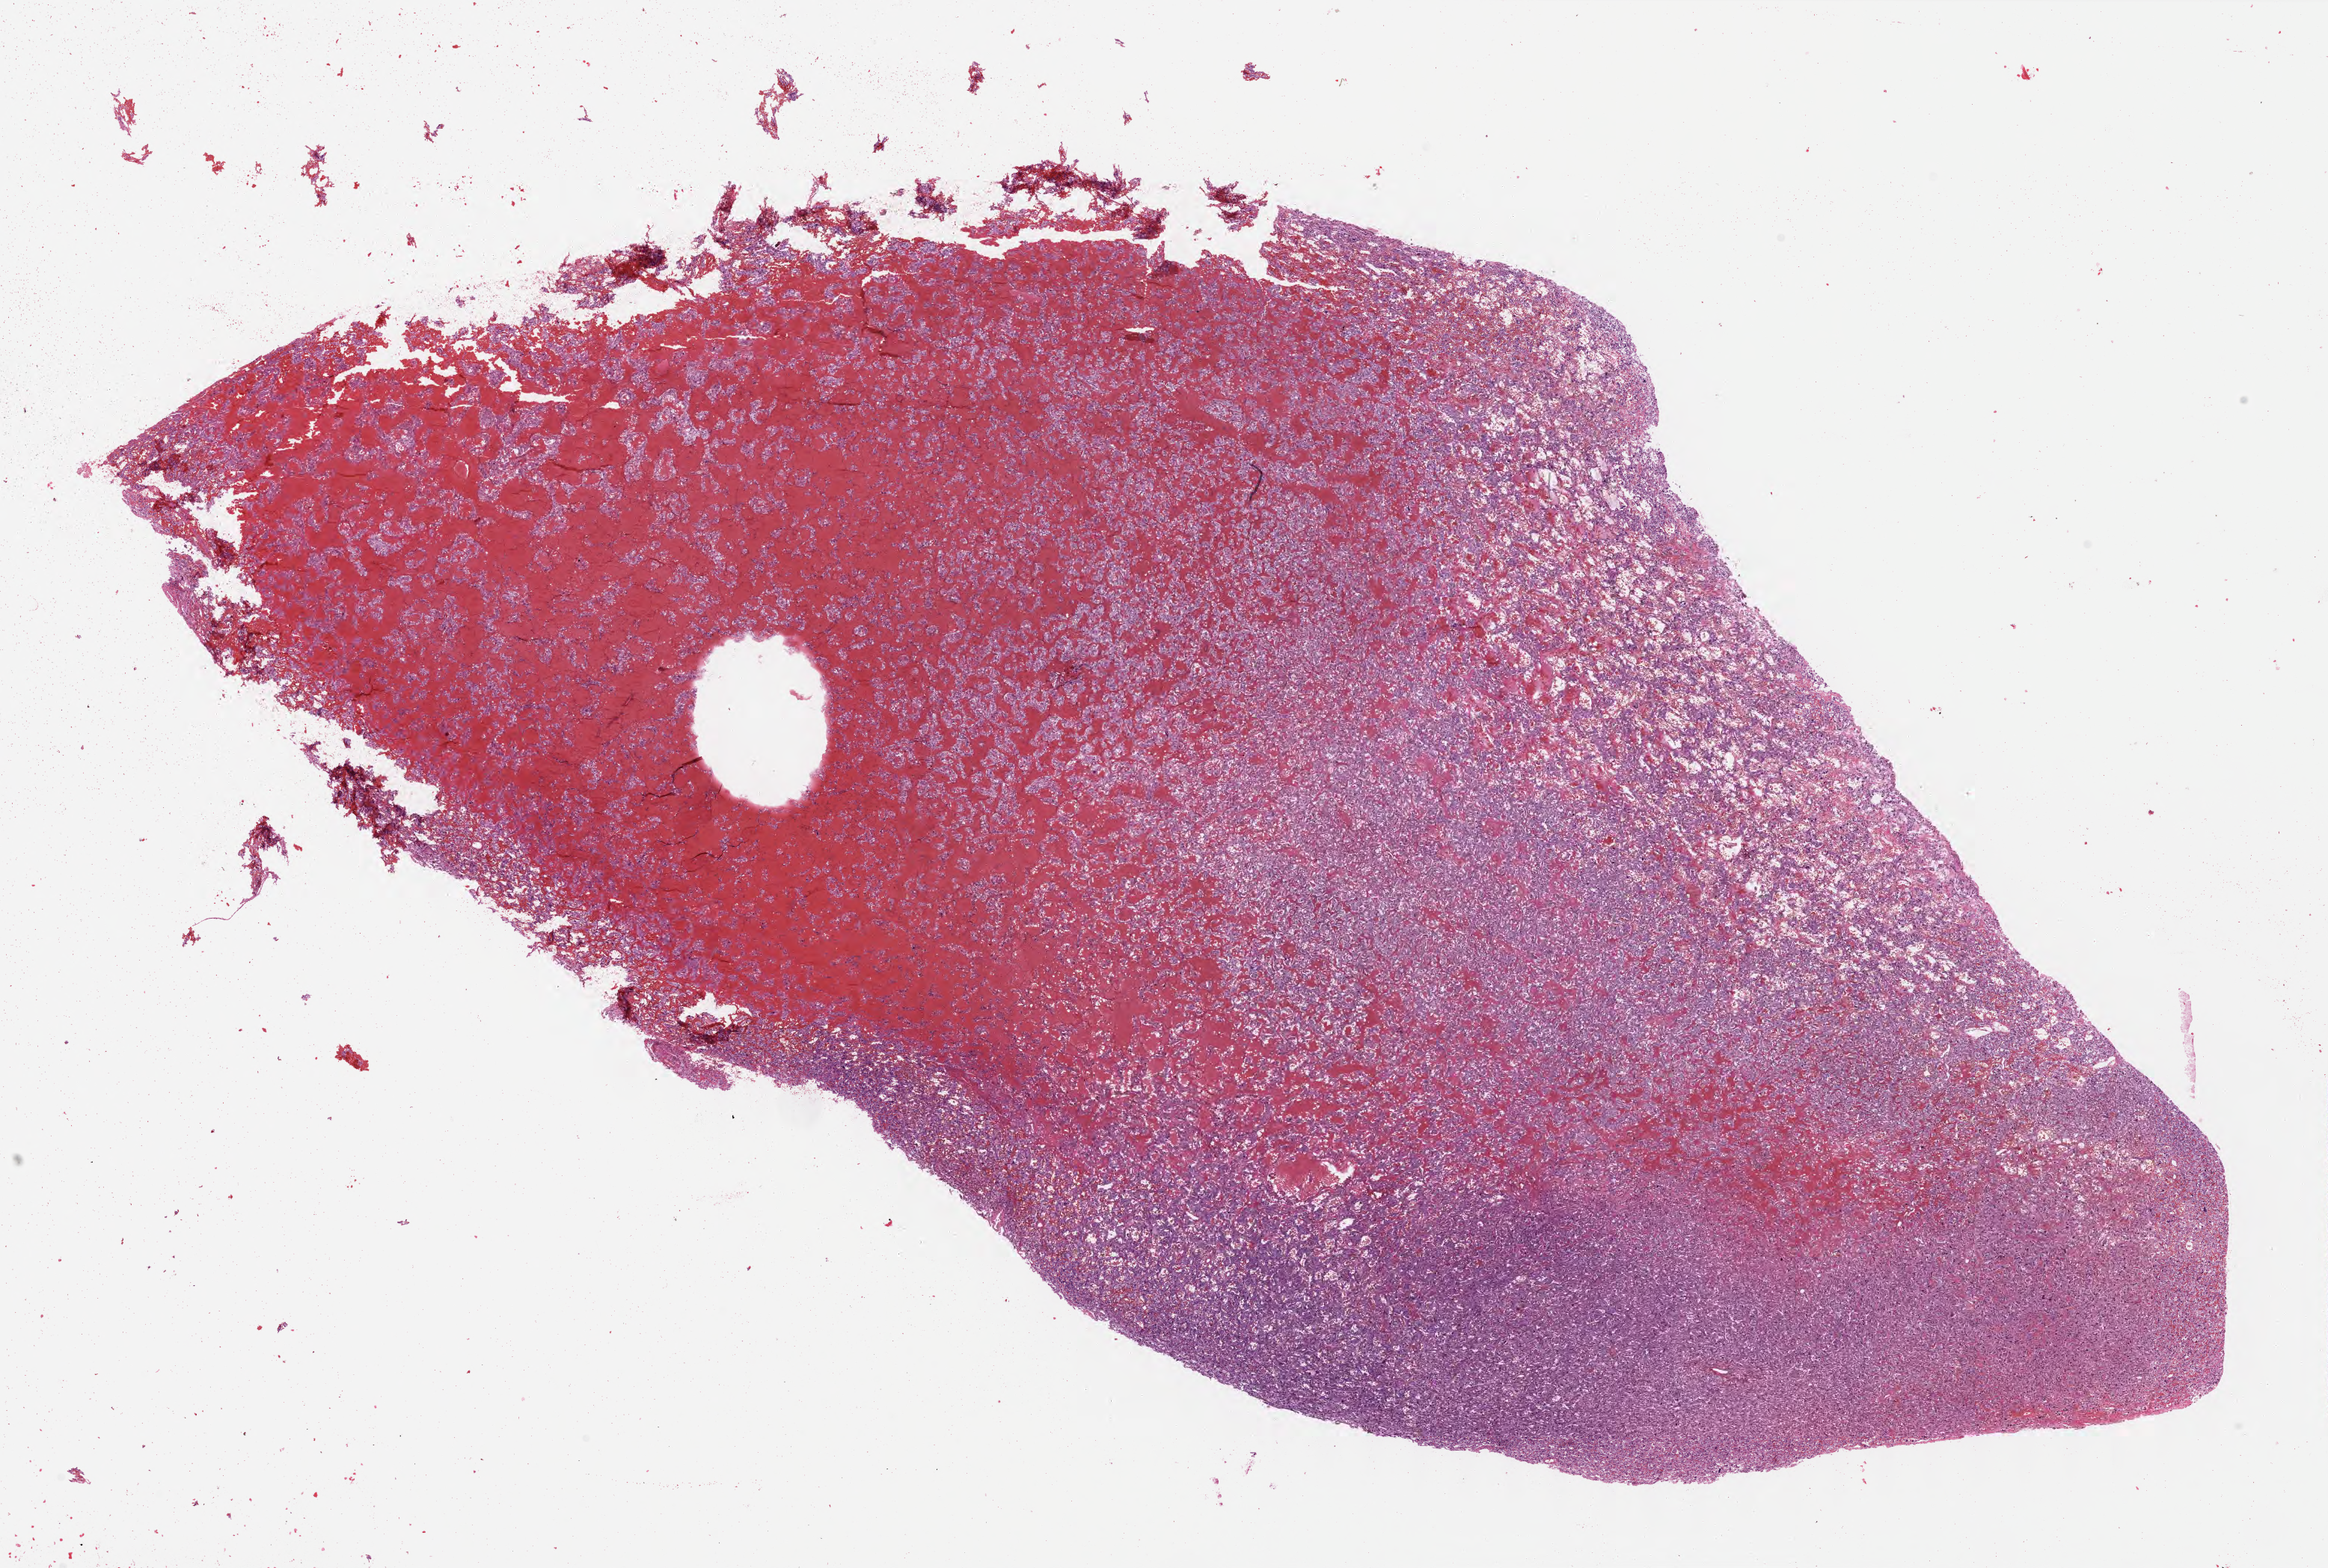
H&E whole-slide image — shown as a low-resolution overview of the whole scanned area (about 24.5 x 16.5 mm, acquisition: 40x scan); formalin-fixed paraffin-embedded (FFPE) diagnostic section; adrenal gland, primary tumour sample. Male, age 31 years at initial diagnosis.
Diagnosis: Pheochromocytoma, NOS.